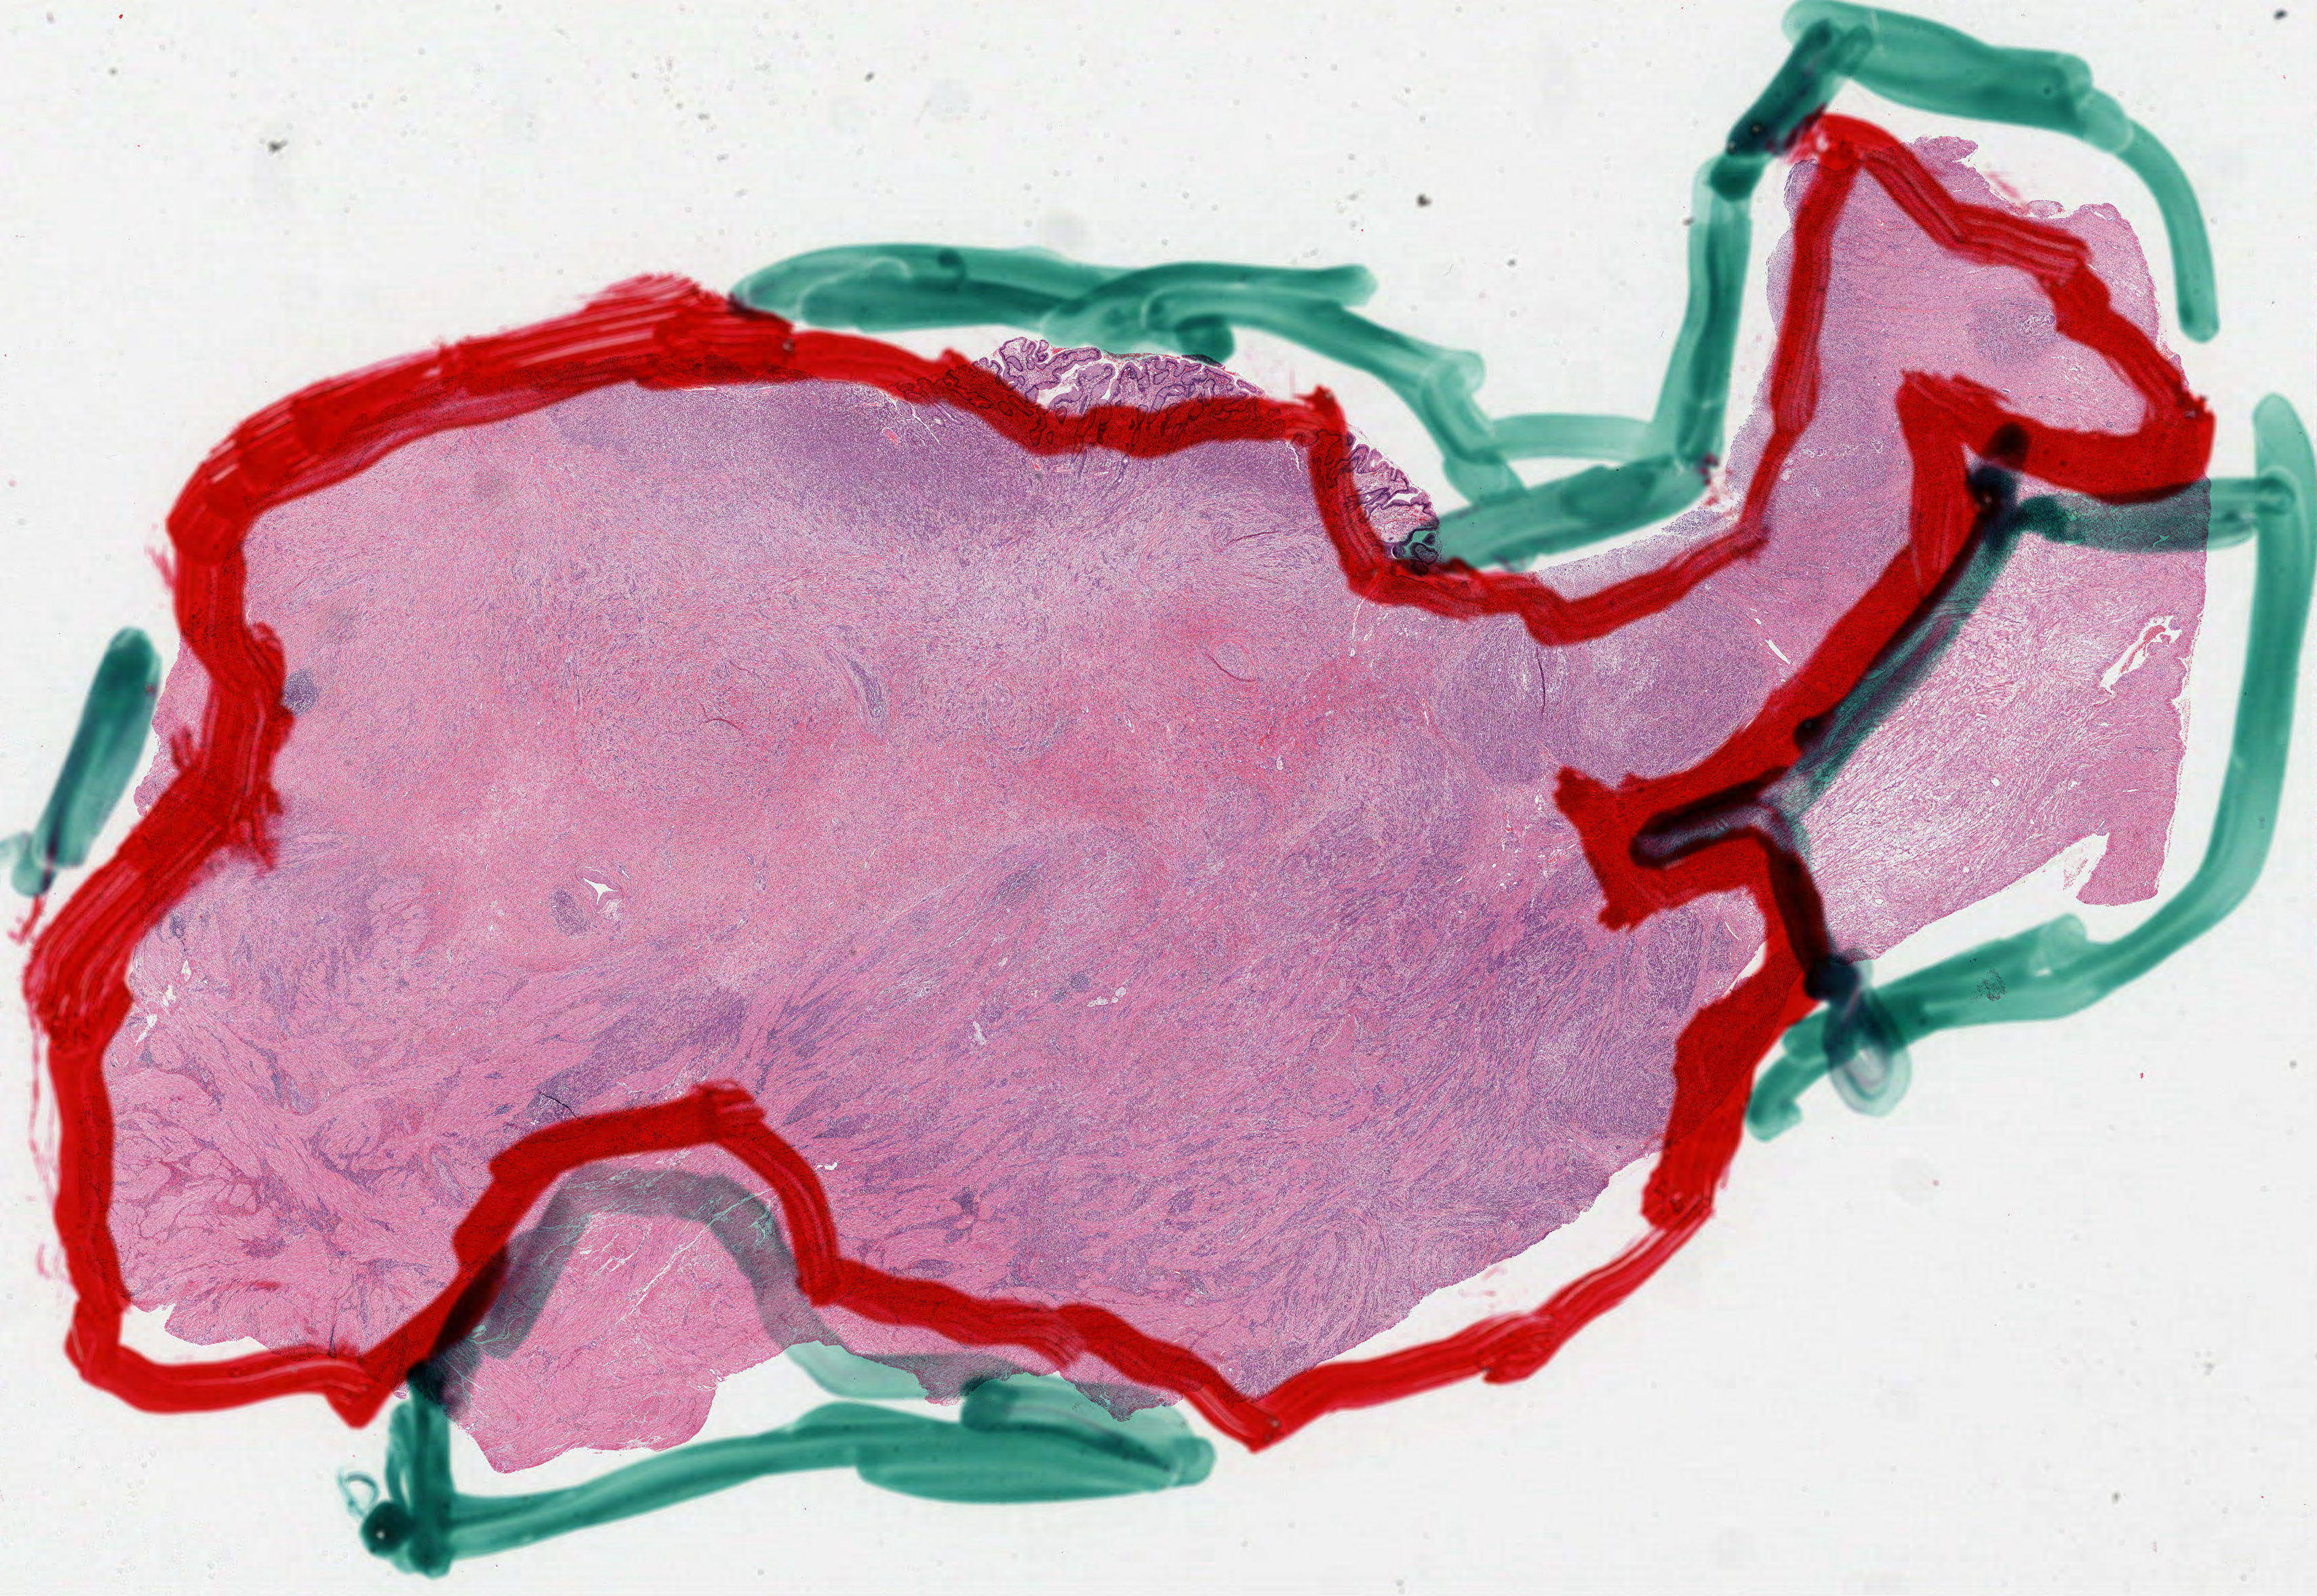
H&E-stained whole-slide image — a low-resolution overview of the entire scanned area, about 27.6 x 19.0 mm, FFPE section, primary tumour sample from the stomach. Female patient; age at initial diagnosis 50 years. Histologic grade: GX (grade cannot be assessed).
Diagnosis: Adenocarcinoma, intestinal type. AJCC pathologic stage: IV (7th edition). Lymph nodes positive (case pathology): 7 of 8 examined. TNM: T3 N3a M1.